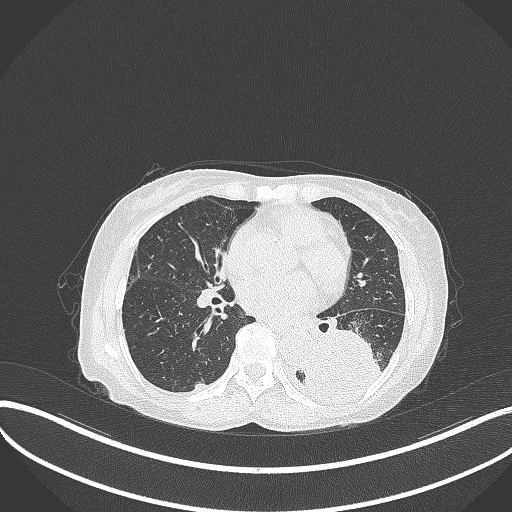
Chest CT, one axial slice. Slice 142 of 370 in the series (ordered by position). Reconstruction kernel B70f. Lung window (W 1500 / L -600 HU). 1 mm slice thickness. 512 × 512 image matrix, field of view 400 × 400 mm. Patient: female, 78 years. Case-level facts recorded for this patient, not image findings: clinical TNM (as recorded): T3 N0 M1.
Outlined on this slice (bounding box drawn by a radiologist):
- lung tumour (recorded histology: squamous cell carcinoma): bounding box (x1, y1, x2, y2) in pixels: (299, 319, 387, 408)